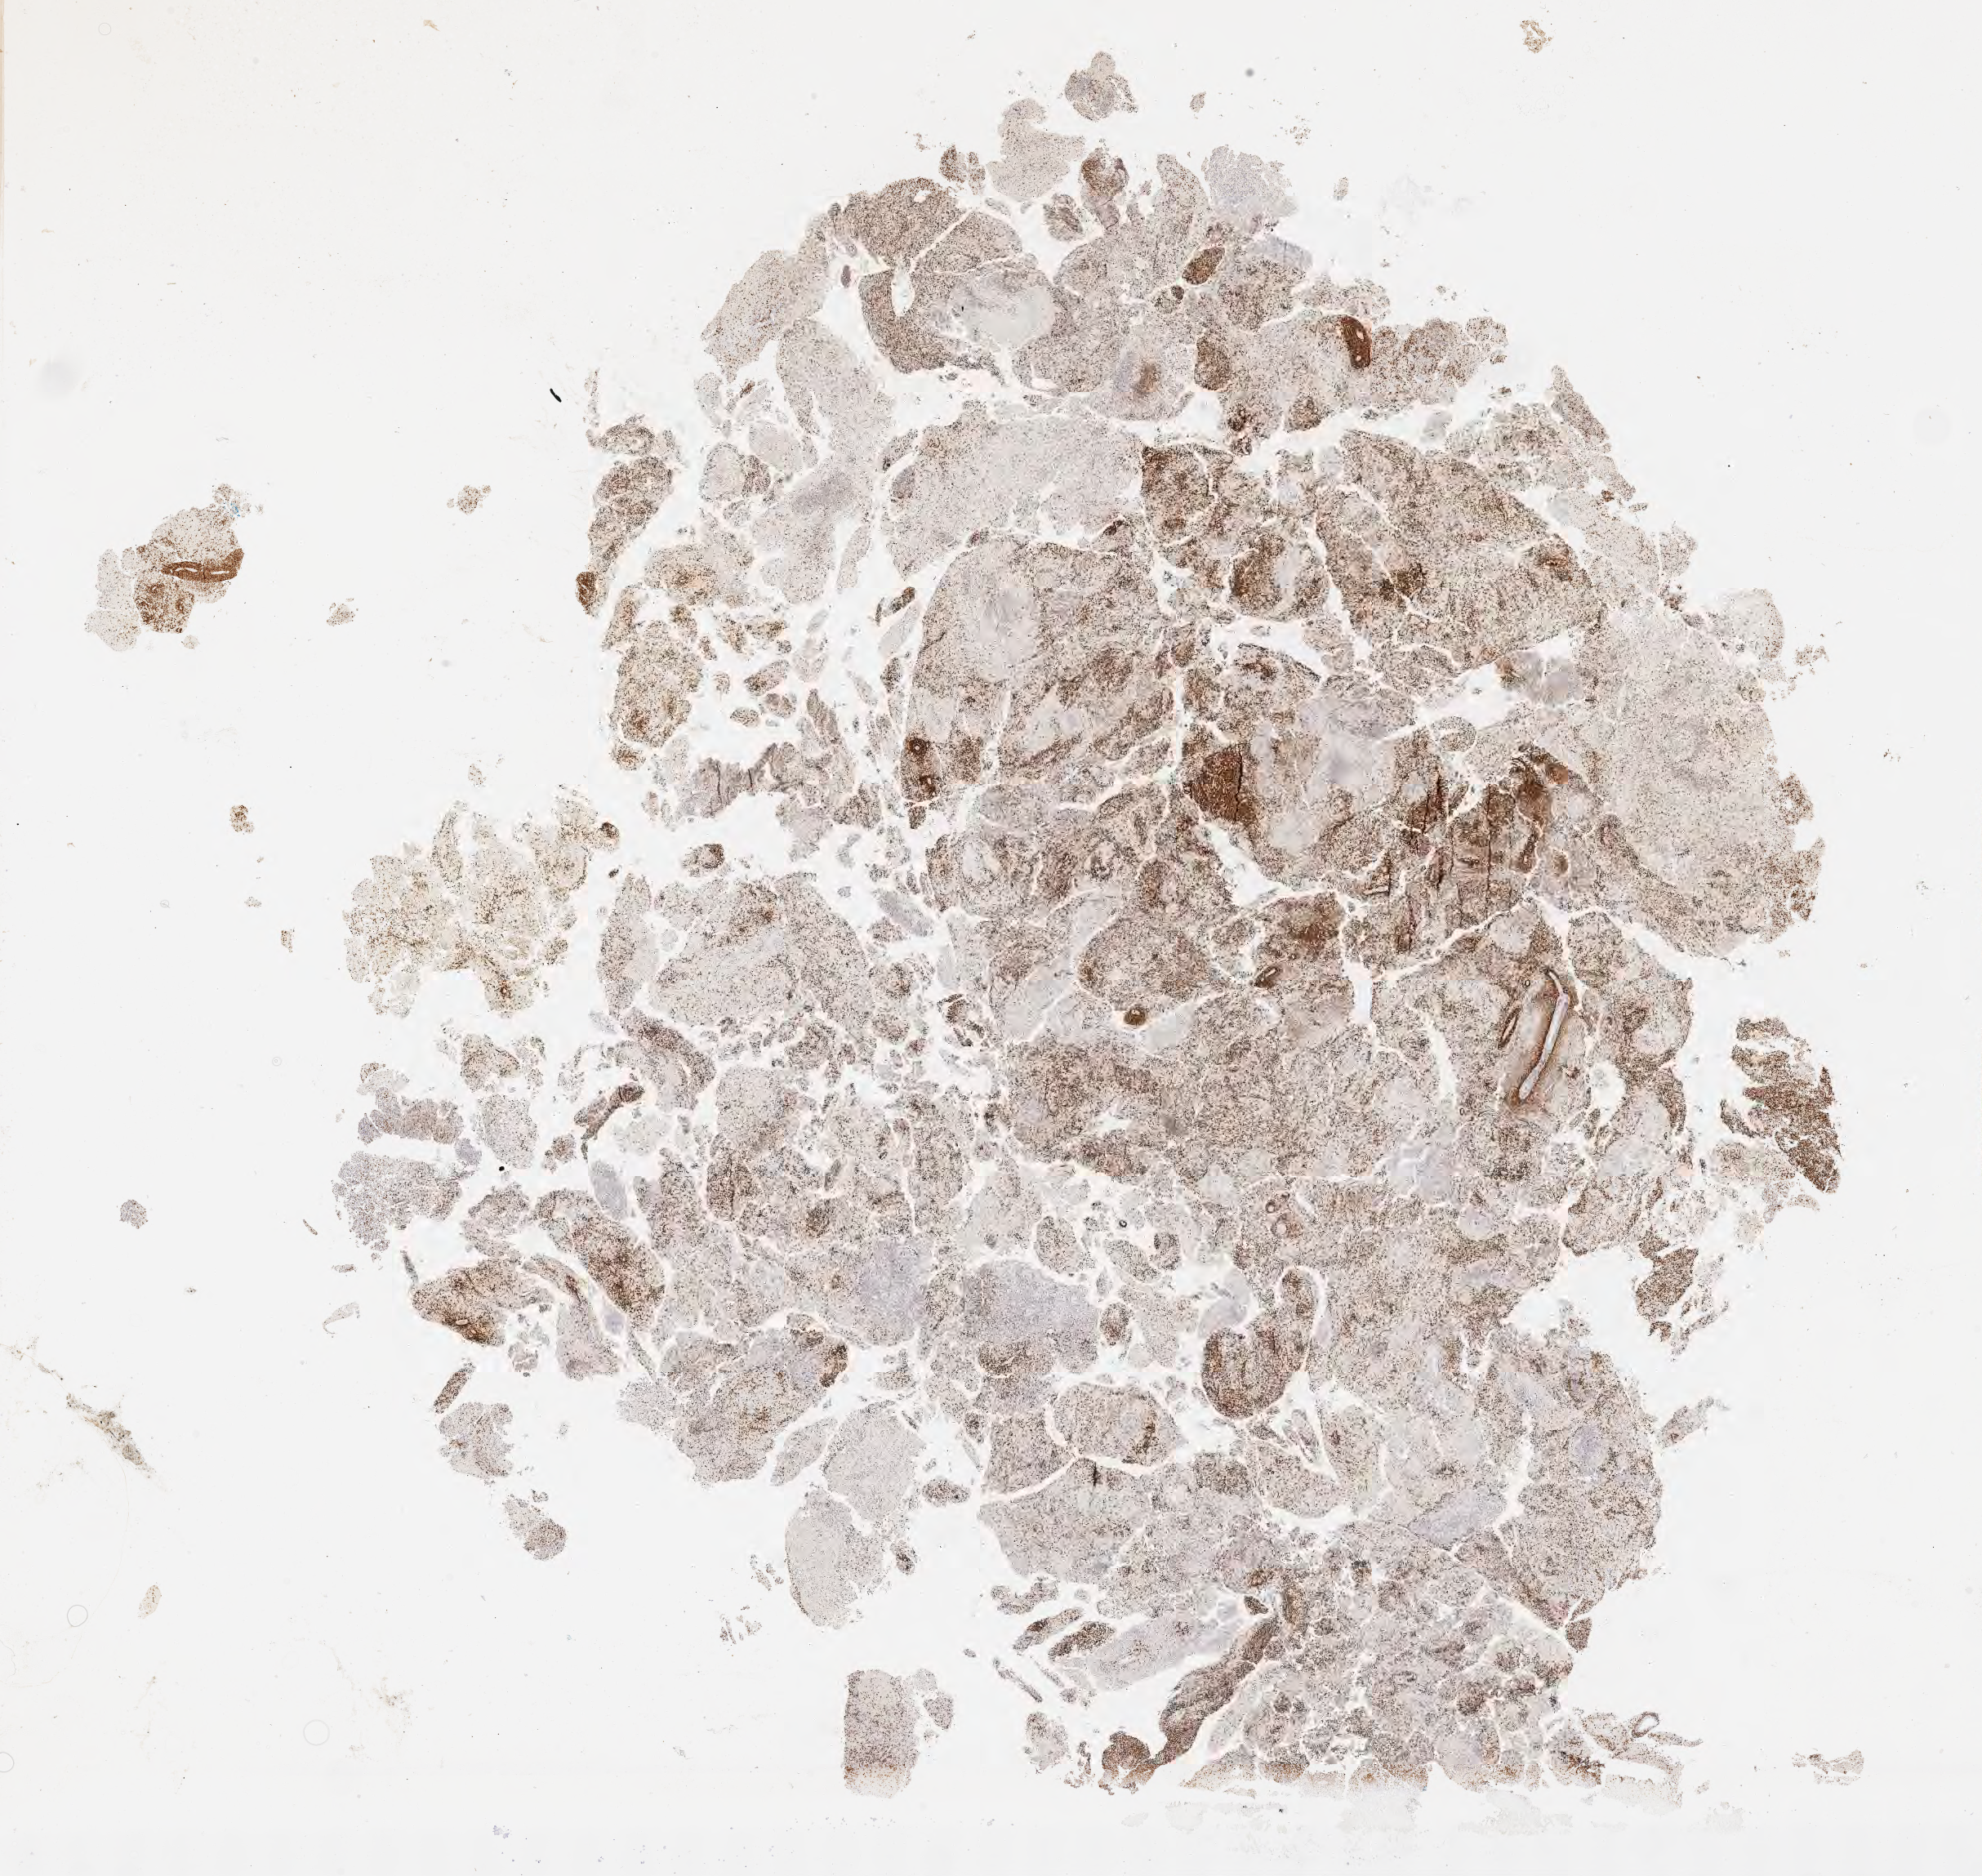
Whole-slide image, immunohistochemical stain for IRF4/MUM1, whole scanned area (about 19.6 x 18.6 mm) shown as a low-resolution overview, specimen: tumor tissue, anatomic site: brain. Male patient, age 51 years.
Histologic diagnosis: Diffuse large B-cell lymphoma, NOS.